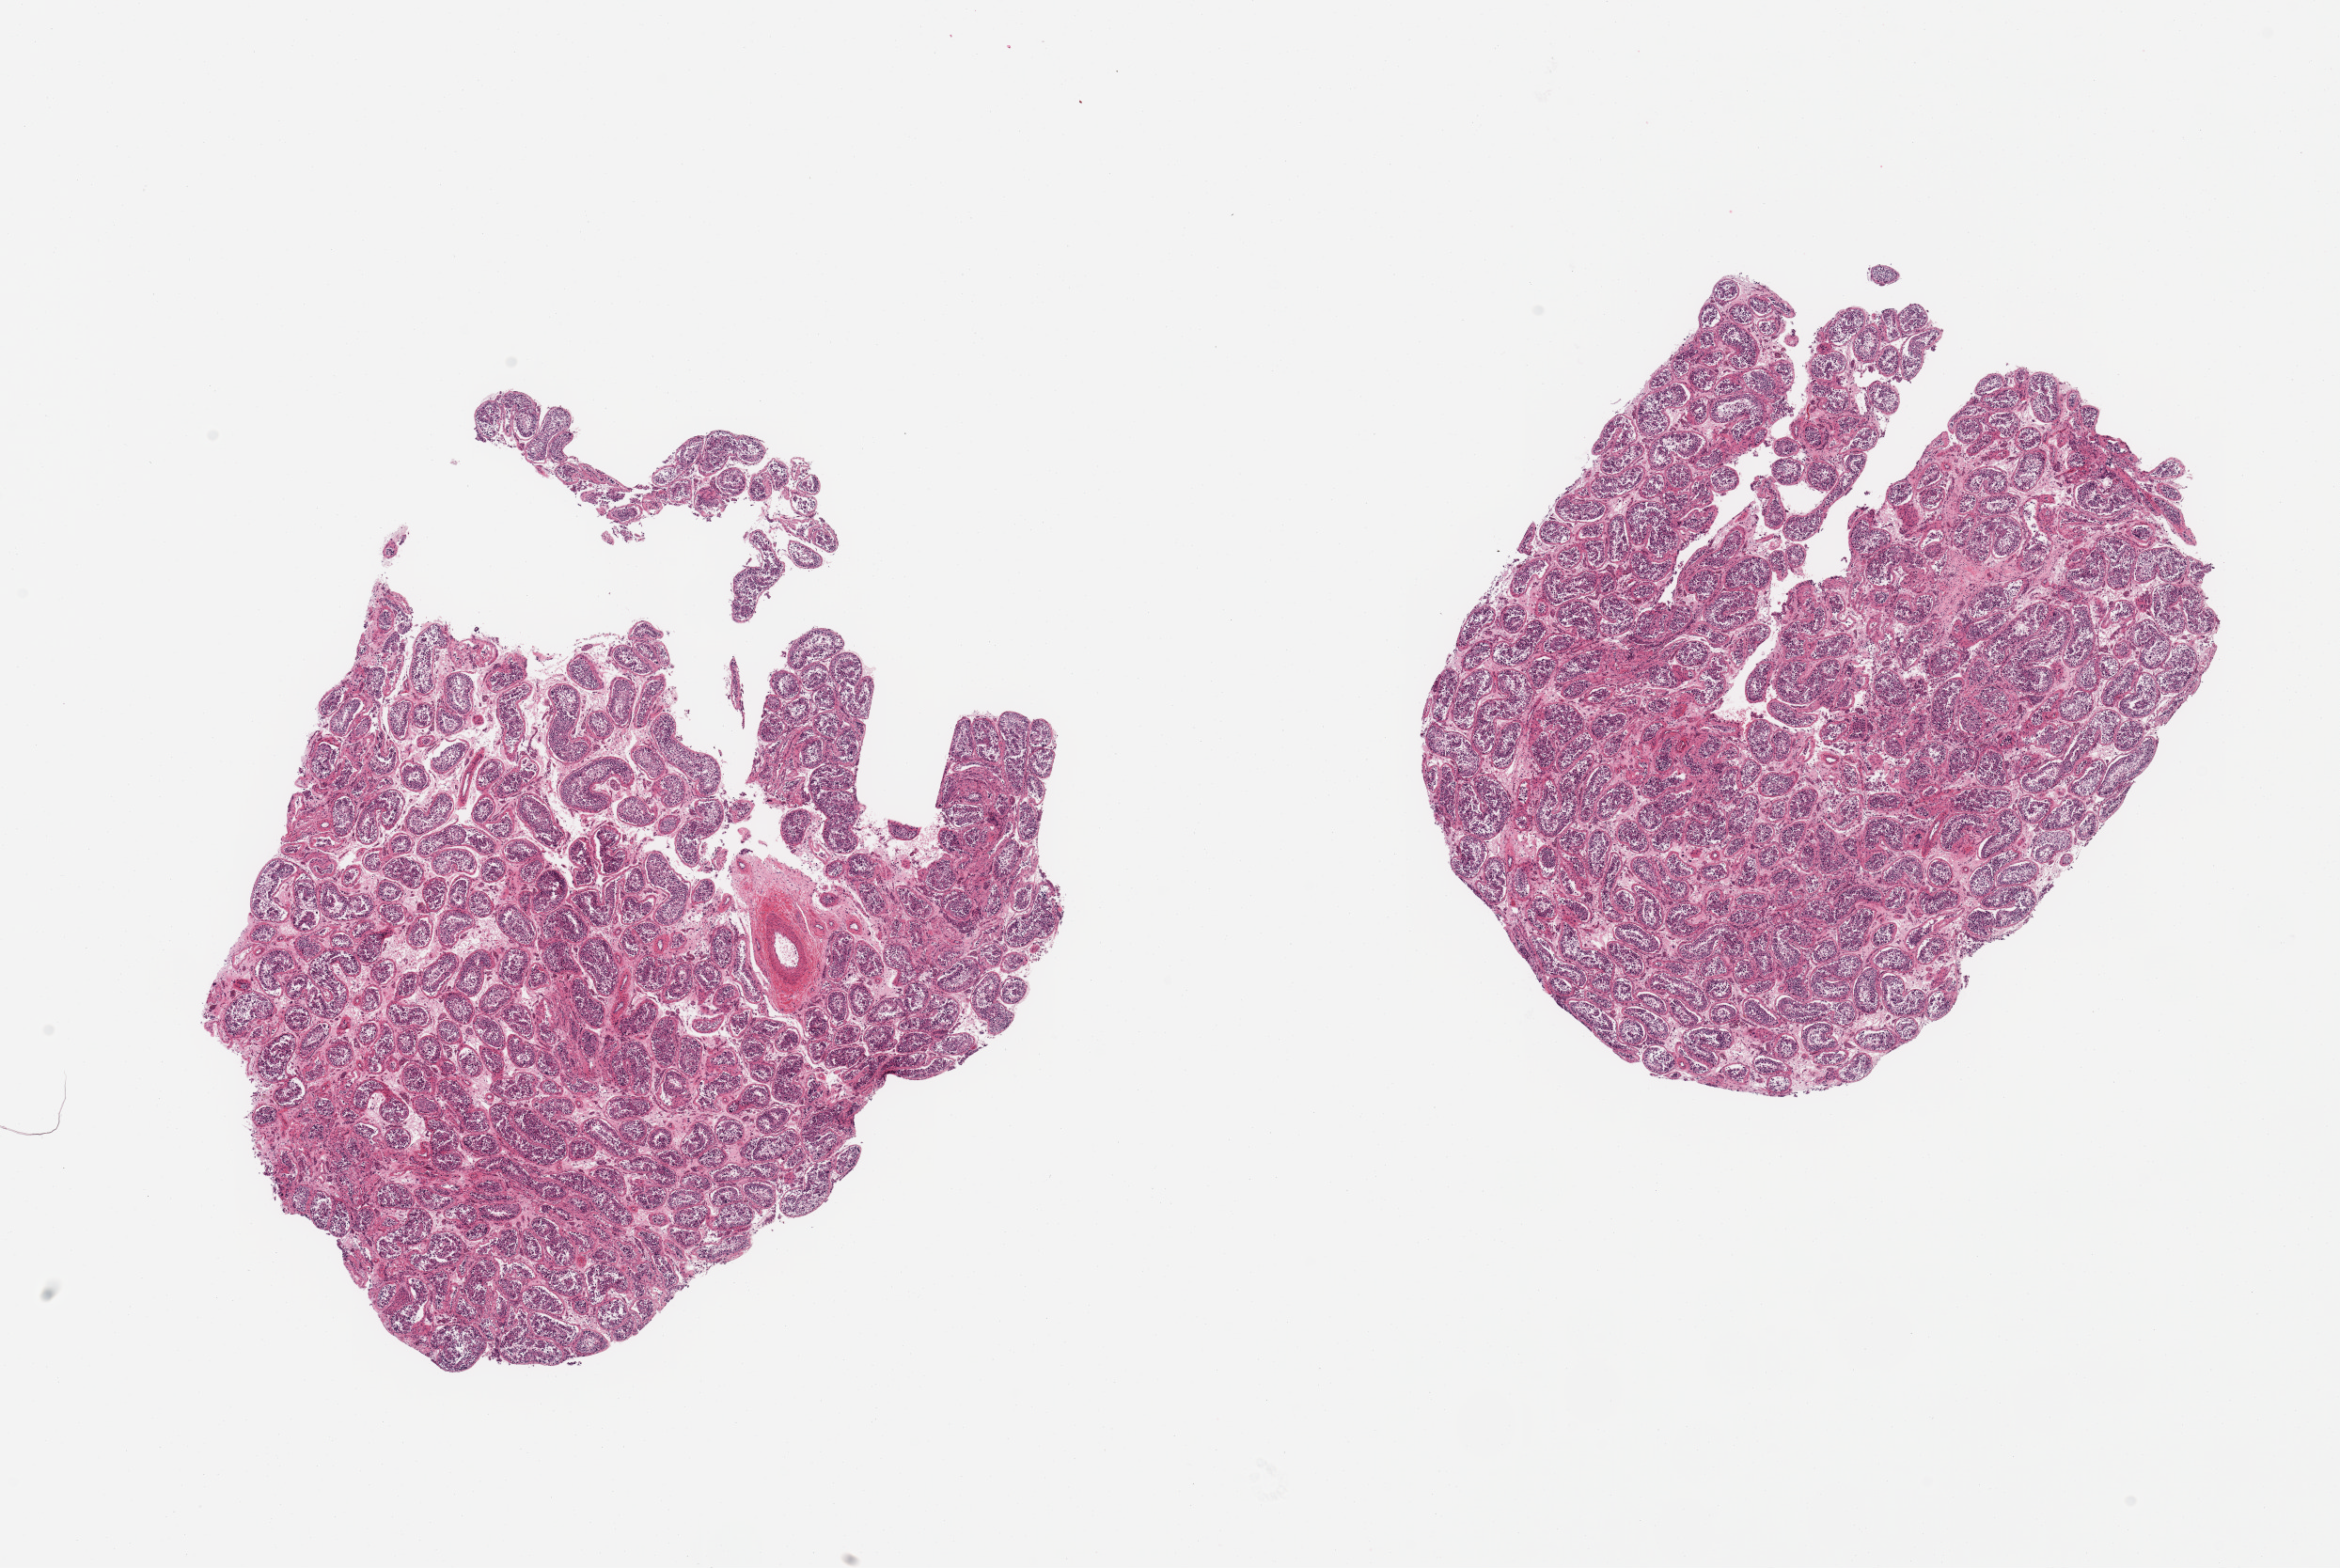
Hematoxylin and eosin (H&E) whole-slide image, low-resolution overview of the scanned area, about 19.7 x 13.2 mm. PAXgene-fixed, paraffin-embedded tissue. Section of testis (target tissue). Tissue donor sample. Donor: male.
Reviewer comment on this tissue sample: 2 pieces; spermatogenesis preserved.